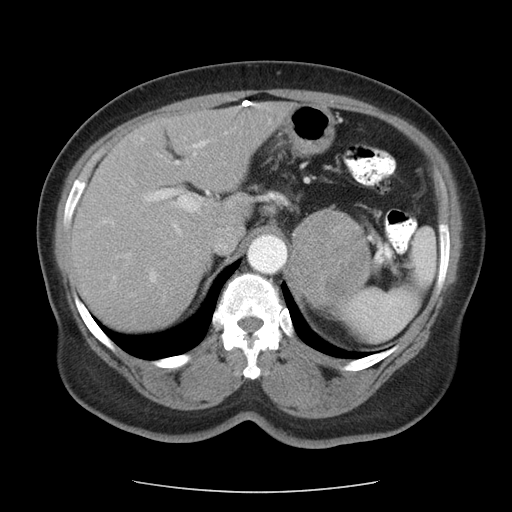
Contrast-enhanced abdominal CT, one axial slice; slice 71 of 95 in the series (ordered by position); intravenous contrast given; soft-tissue window (W 400 / L 40 HU); 512 × 512 image matrix, field of view 362 × 362 mm. Female patient, age 71 years. Case-level facts recorded for this patient, not image findings: diagnosis: adrenocortical carcinoma; tumour side: left adrenal; tumour size at pathology: 8.8 cm; Ki-67 index: 20 %; stage (as recorded): 2.
Structures marked on this image (semi-automatically segmented with operator editing):
- mass: bounding box [x1, y1, x2, y2] px = [289, 209, 369, 306]